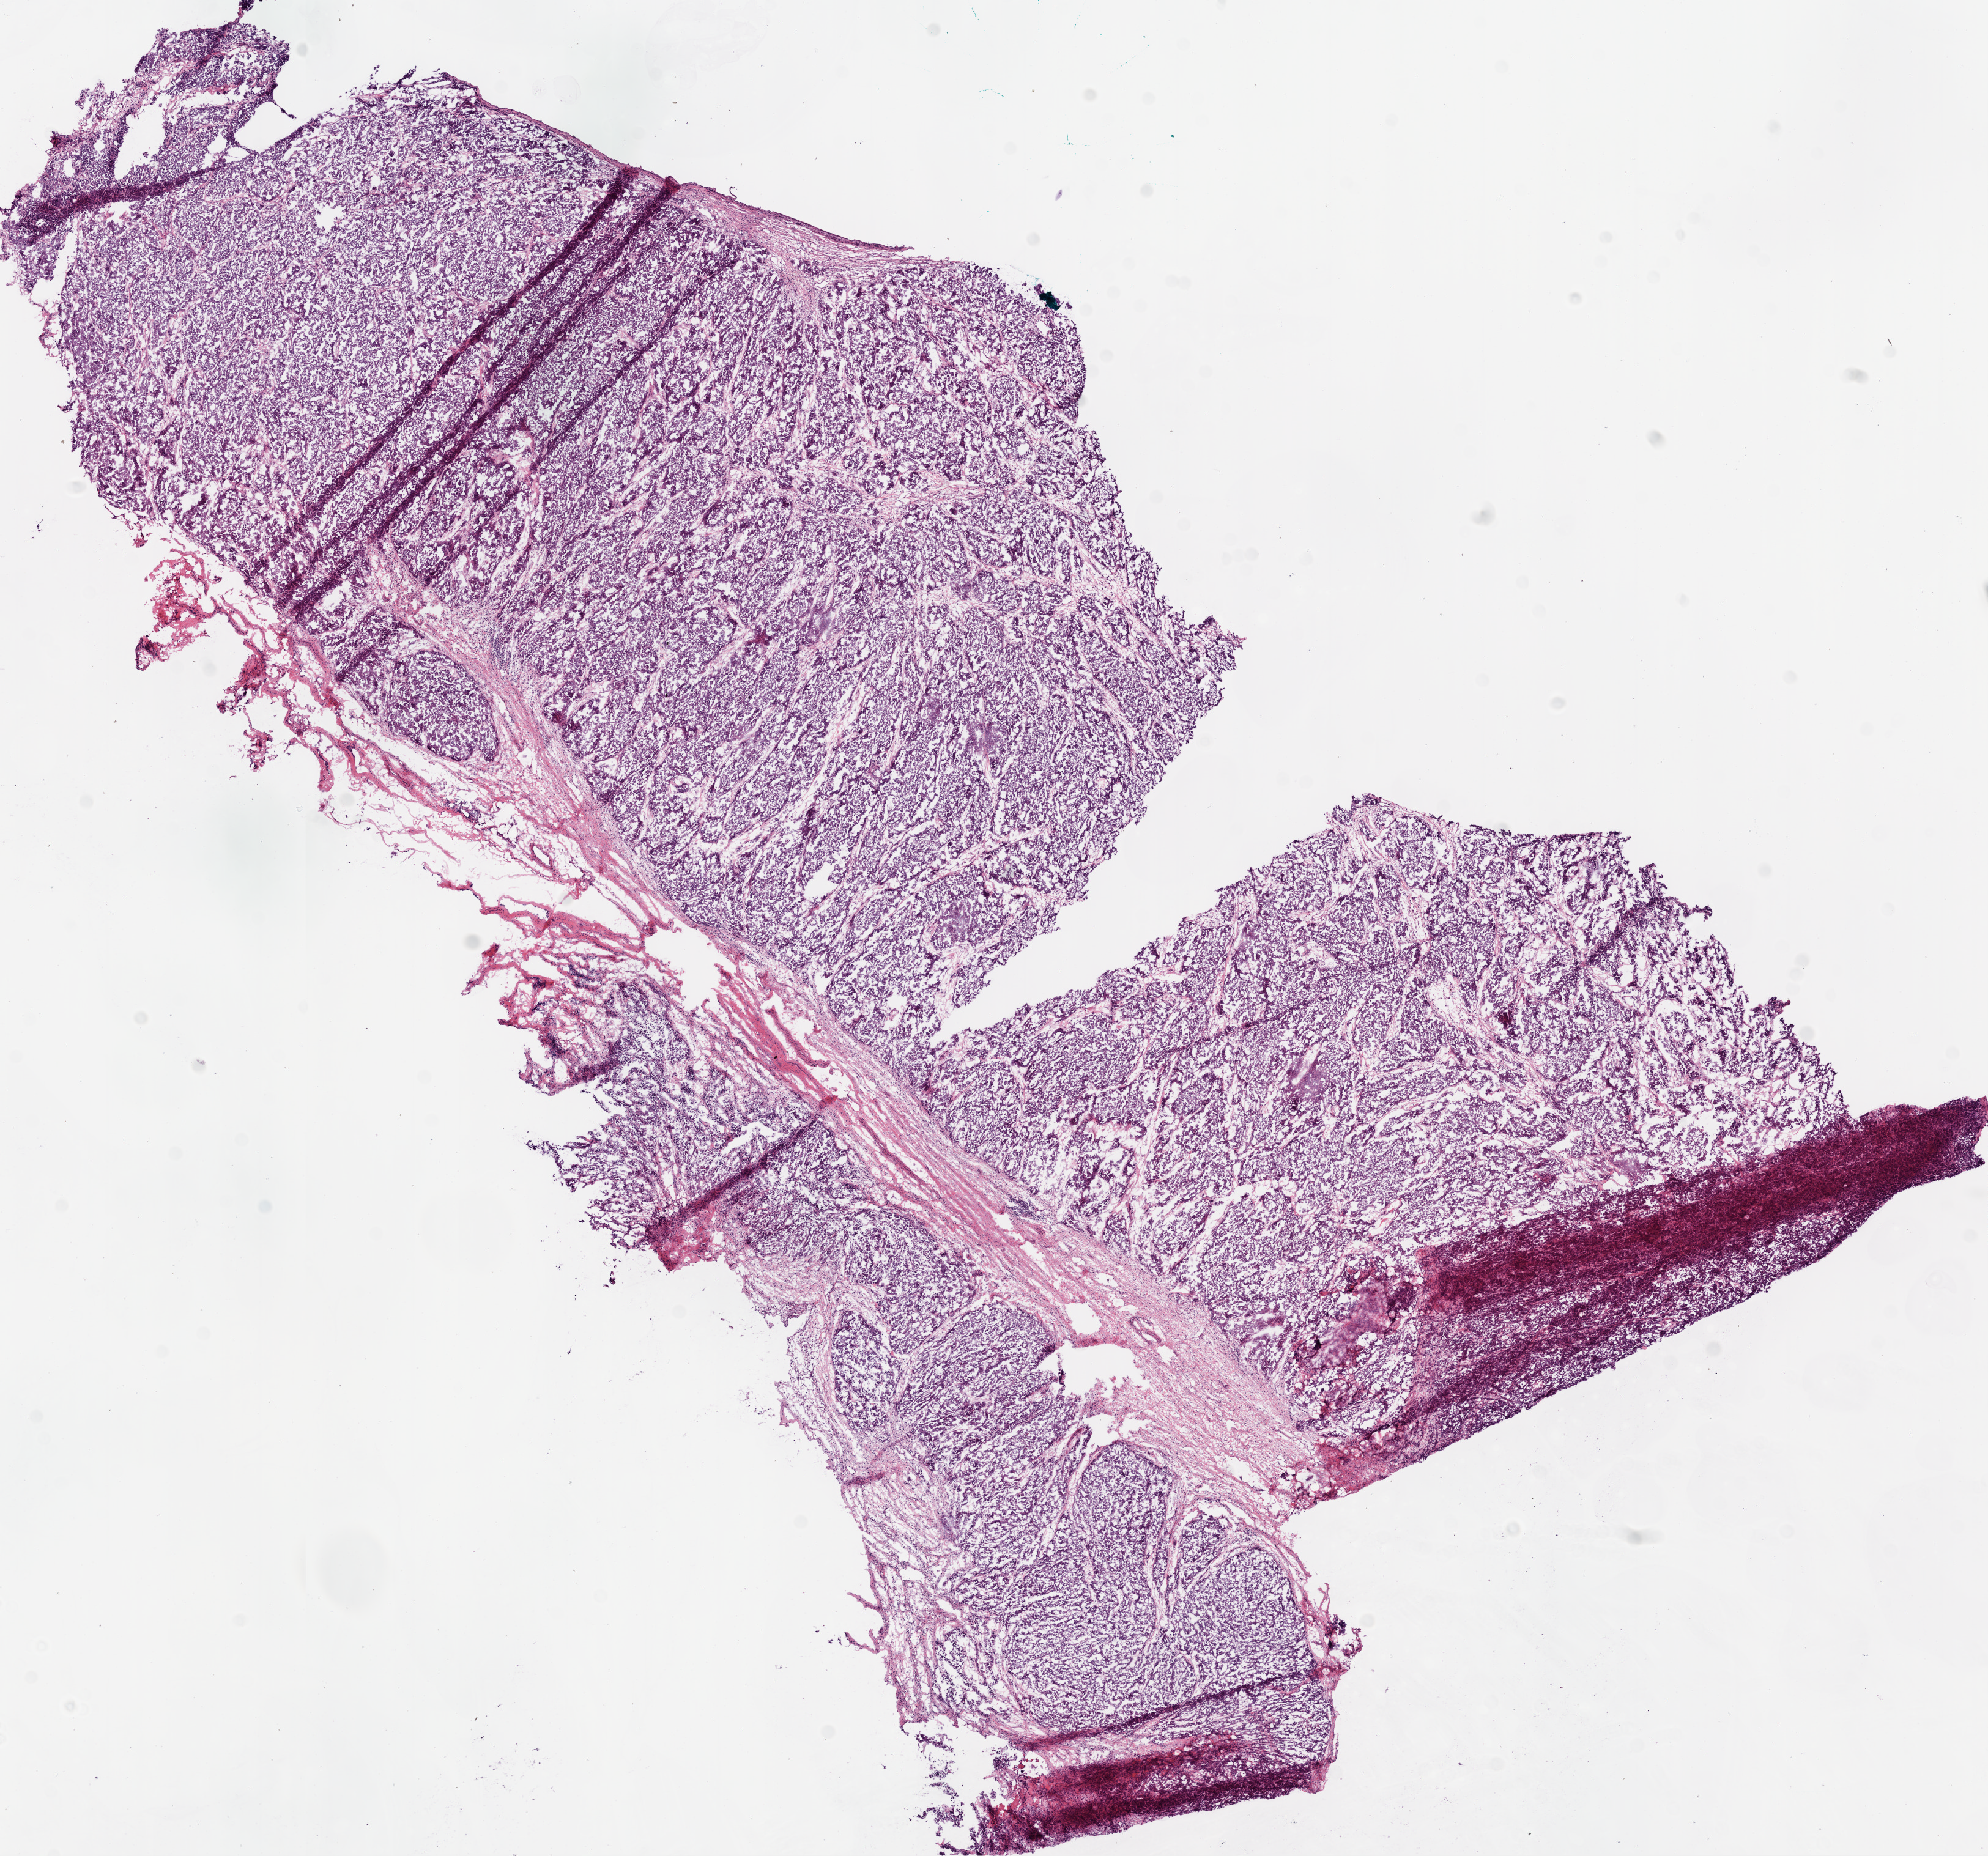
Hematoxylin and eosin (H&E) stained whole-slide image — shown as a low-resolution overview of the whole scanned area (about 13.0 x 12.2 mm, slide scanned at 20x), frozen section from the bottom of the tissue portion, primary tumour sample from the ovary. Female, age 67 years at initial diagnosis. Composition of this section per pathologist review: tumour cells 94%, tumour nuclei 95%.
Pathologic diagnosis: Serous cystadenocarcinoma, NOS.